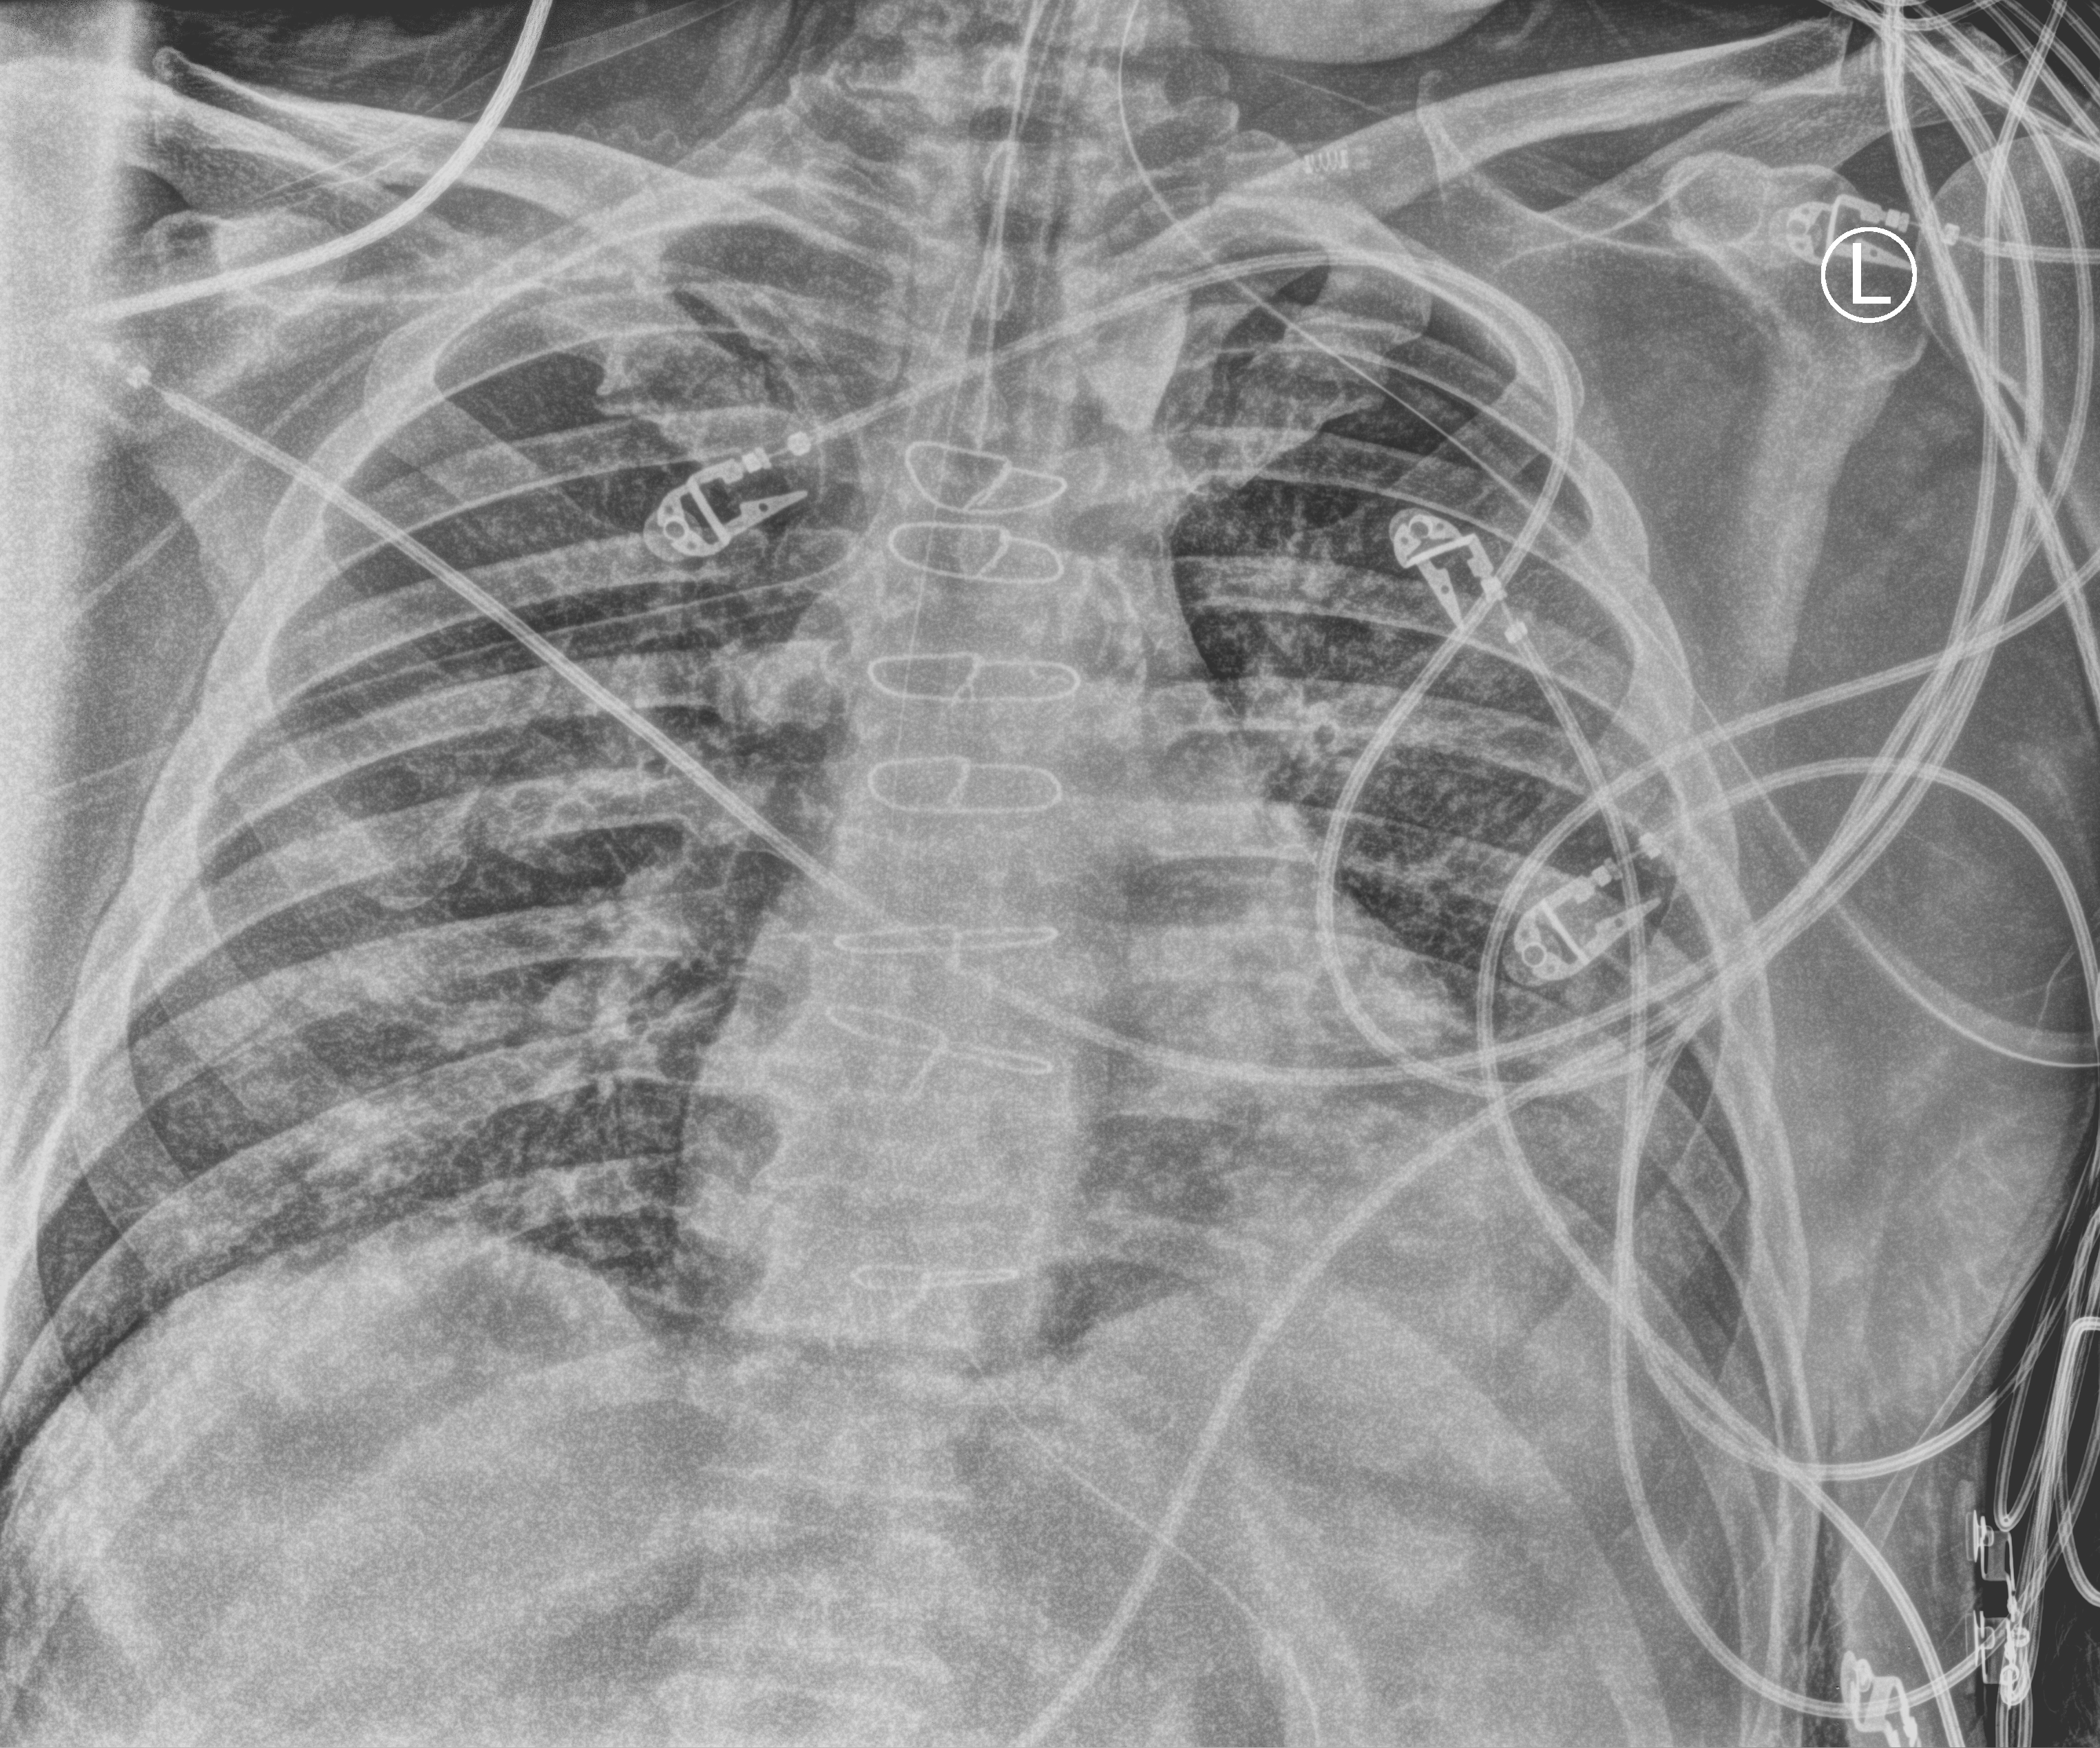
Portable chest radiograph, anteroposterior (AP) projection. Male patient hospitalised with COVID-19, age 60–74 years.
Admission-level facts for this patient (not findings on this image; timing relative to this image not recorded): admitted to intensive care during this hospital stay: yes.